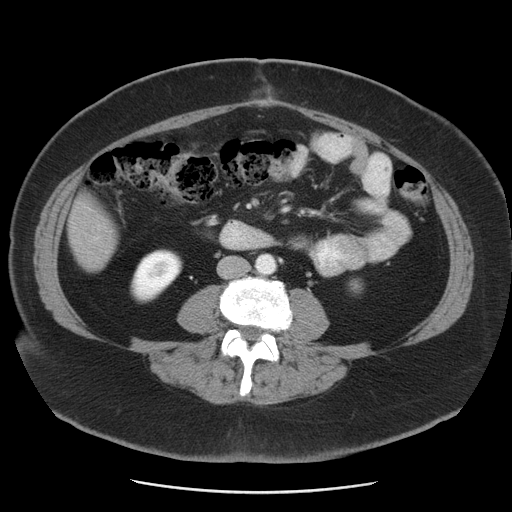
Contrast-enhanced abdominal CT, one axial slice; slice 6 of 55 in the series (ordered by position); reconstruction kernel STANDARD; intravenous contrast given; soft-tissue window (W 400 / L 40 HU); 5 mm slice thickness; 512 × 512 image matrix, field of view 380 × 380 mm. Female patient, age 52 years. Case-level facts recorded for this patient, not image findings: diagnosis: colorectal cancer liver metastases, imaged before liver resection; multiple liver metastases: yes.
Annotated regions visible in this slice (outlined manually by an expert reader):
- liver: bounding box [x1, y1, x2, y2] px = [68, 193, 117, 271]
- planned liver remnant (the part of the liver to remain after resection): [68, 201, 116, 272]
- portal vein (with intrahepatic branches): [93, 236, 100, 241]